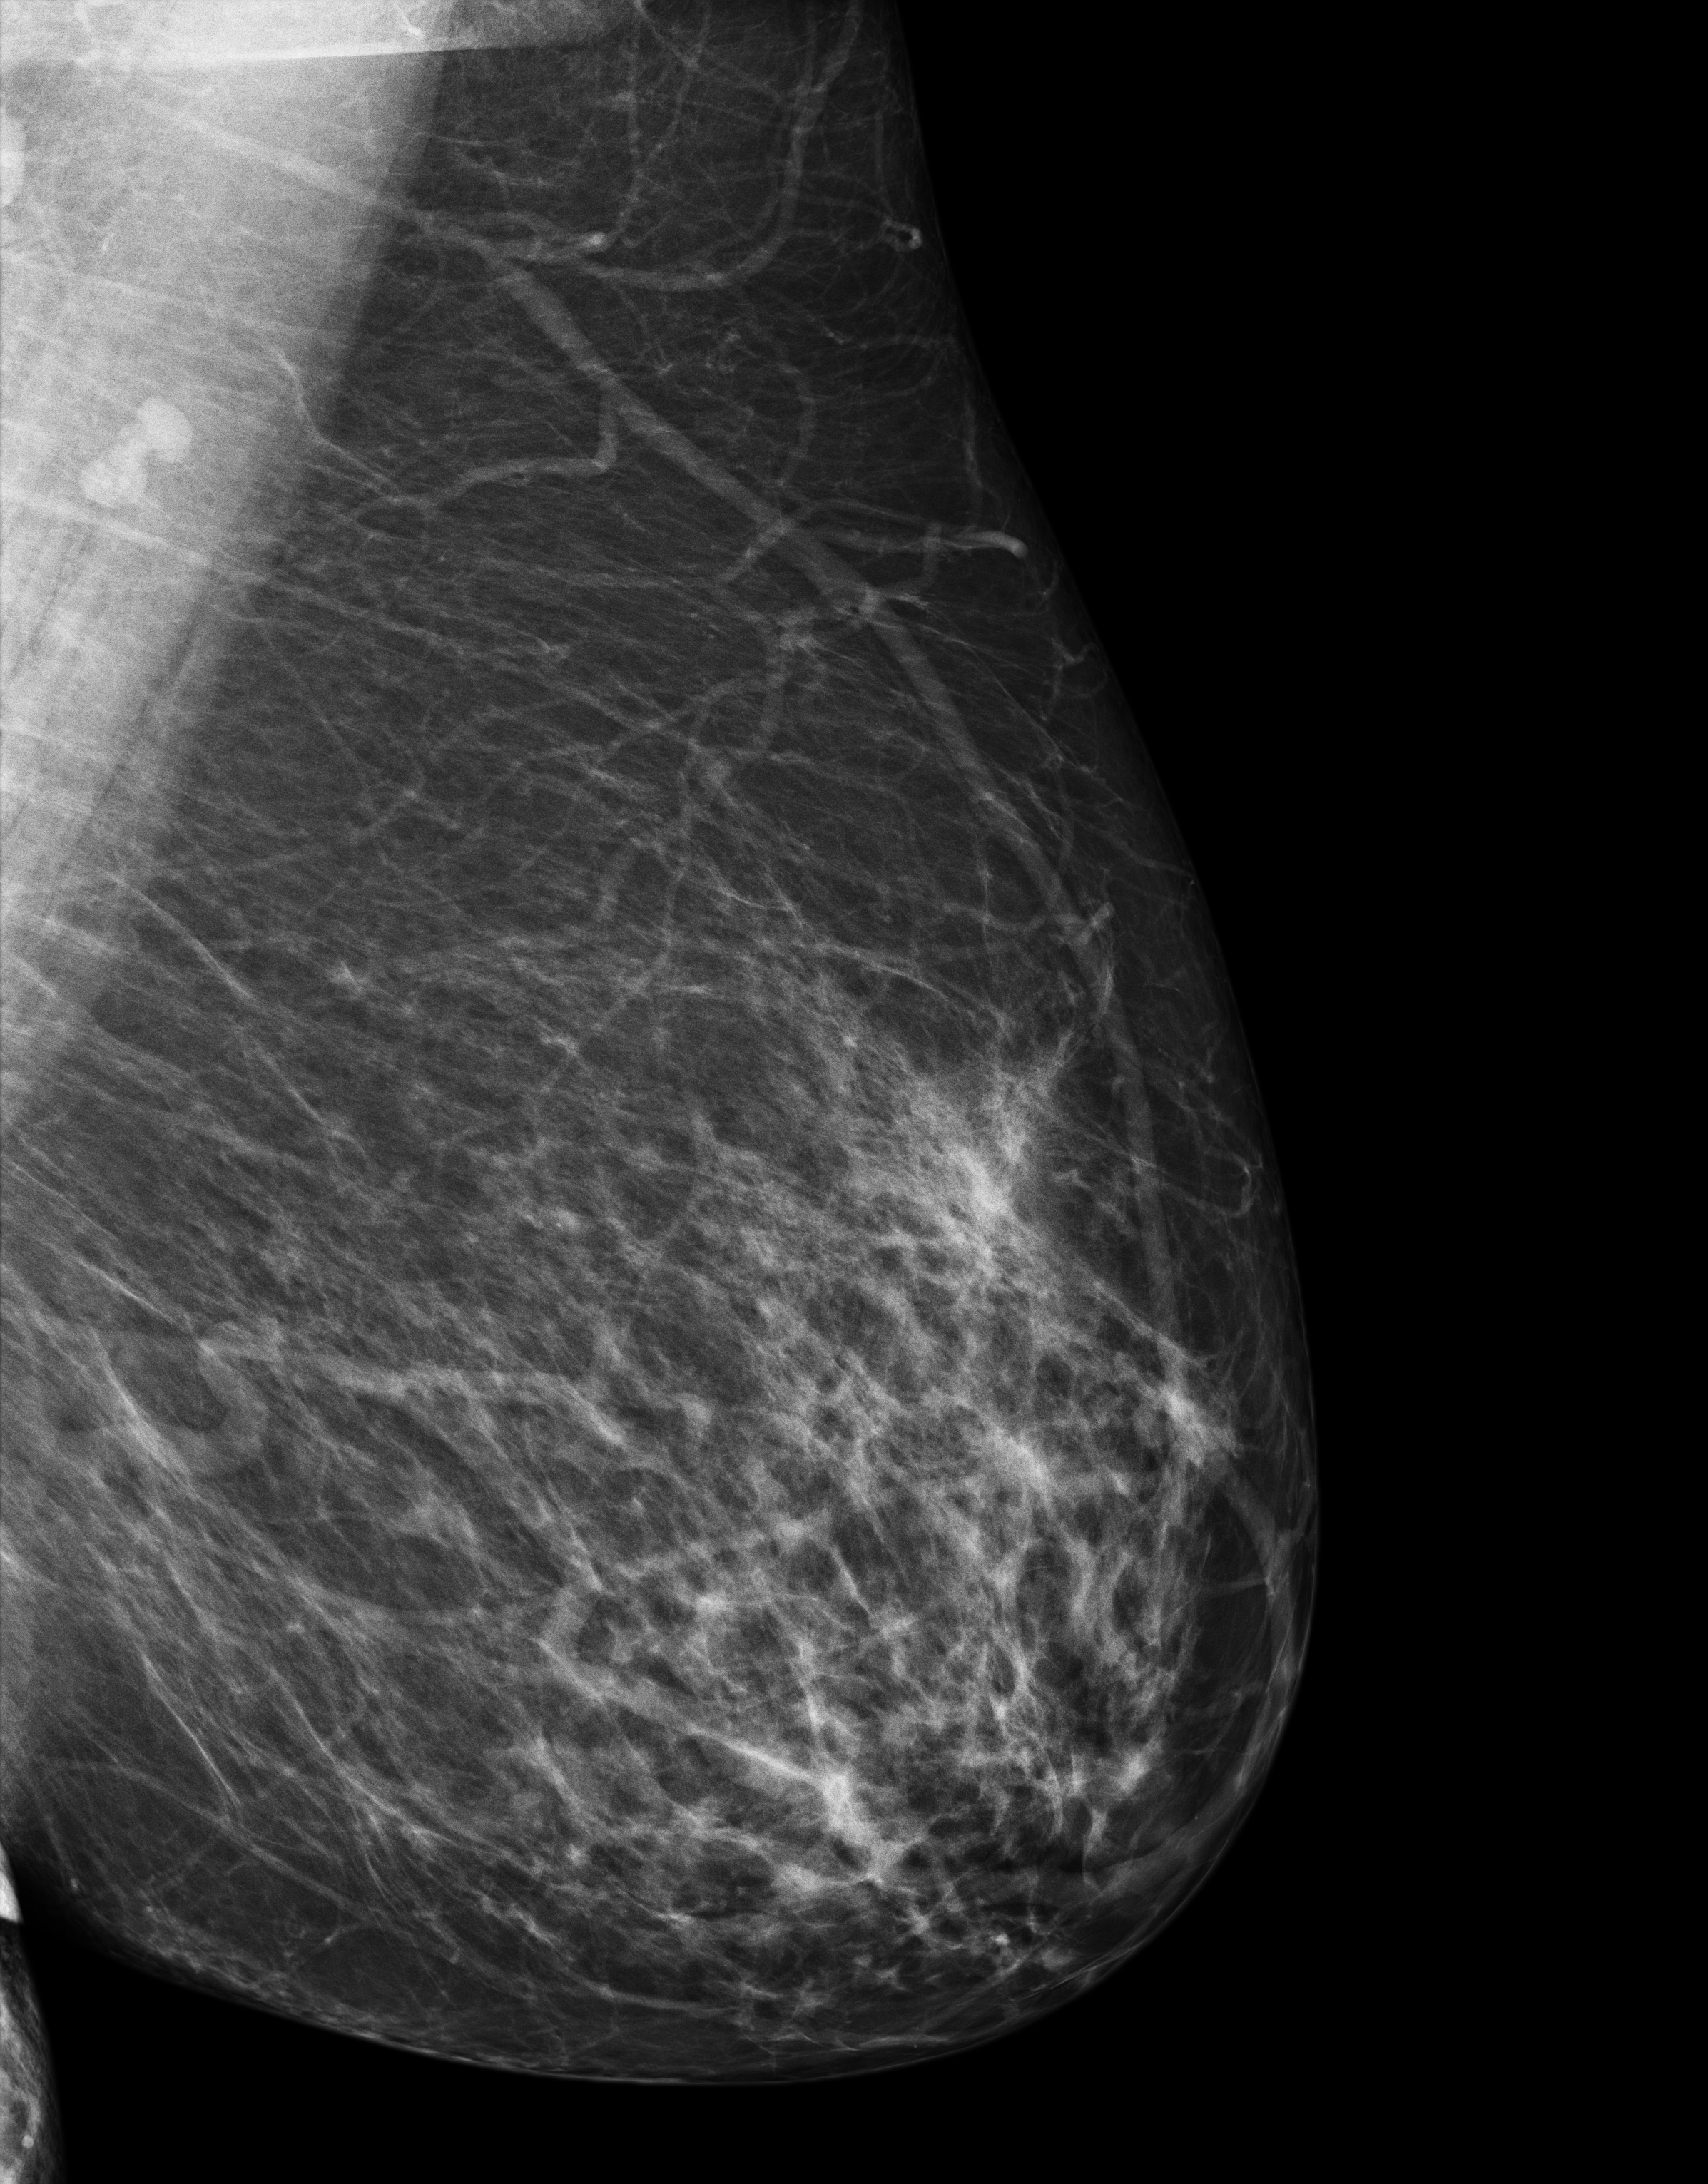
Annual screening mammography examination. Female patient, age 58 years.
Image type: full-field digital mammogram. Breast: left. Projection: MLO view.